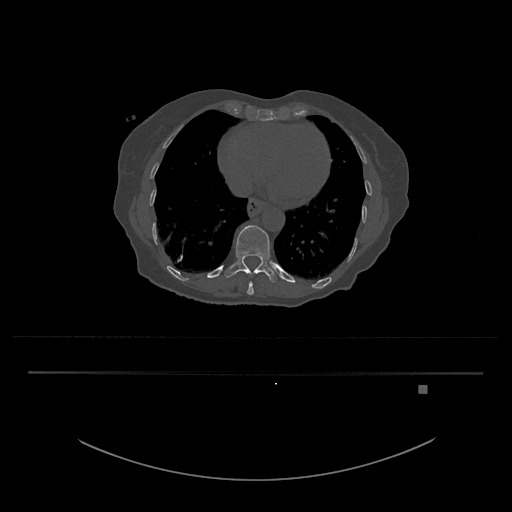
CT including the spine, one axial slice. Slice 678 of 797 in the series (ordered by position). 120 kVp. Bone window (W 1800 / L 400 HU). 512 × 512 image matrix, field of view 500 × 500 mm. Patient: female, 57 years. From the clinical record (not read from this slice): primary cancer: cervical.
Annotated regions visible in this slice (semi-automatic segmentation, software-assisted and operator-edited):
- T10 vertebra: box from (x=247, y=272) to (x=254, y=295) px
- T11 vertebra: (x=224, y=225)–(x=277, y=282)